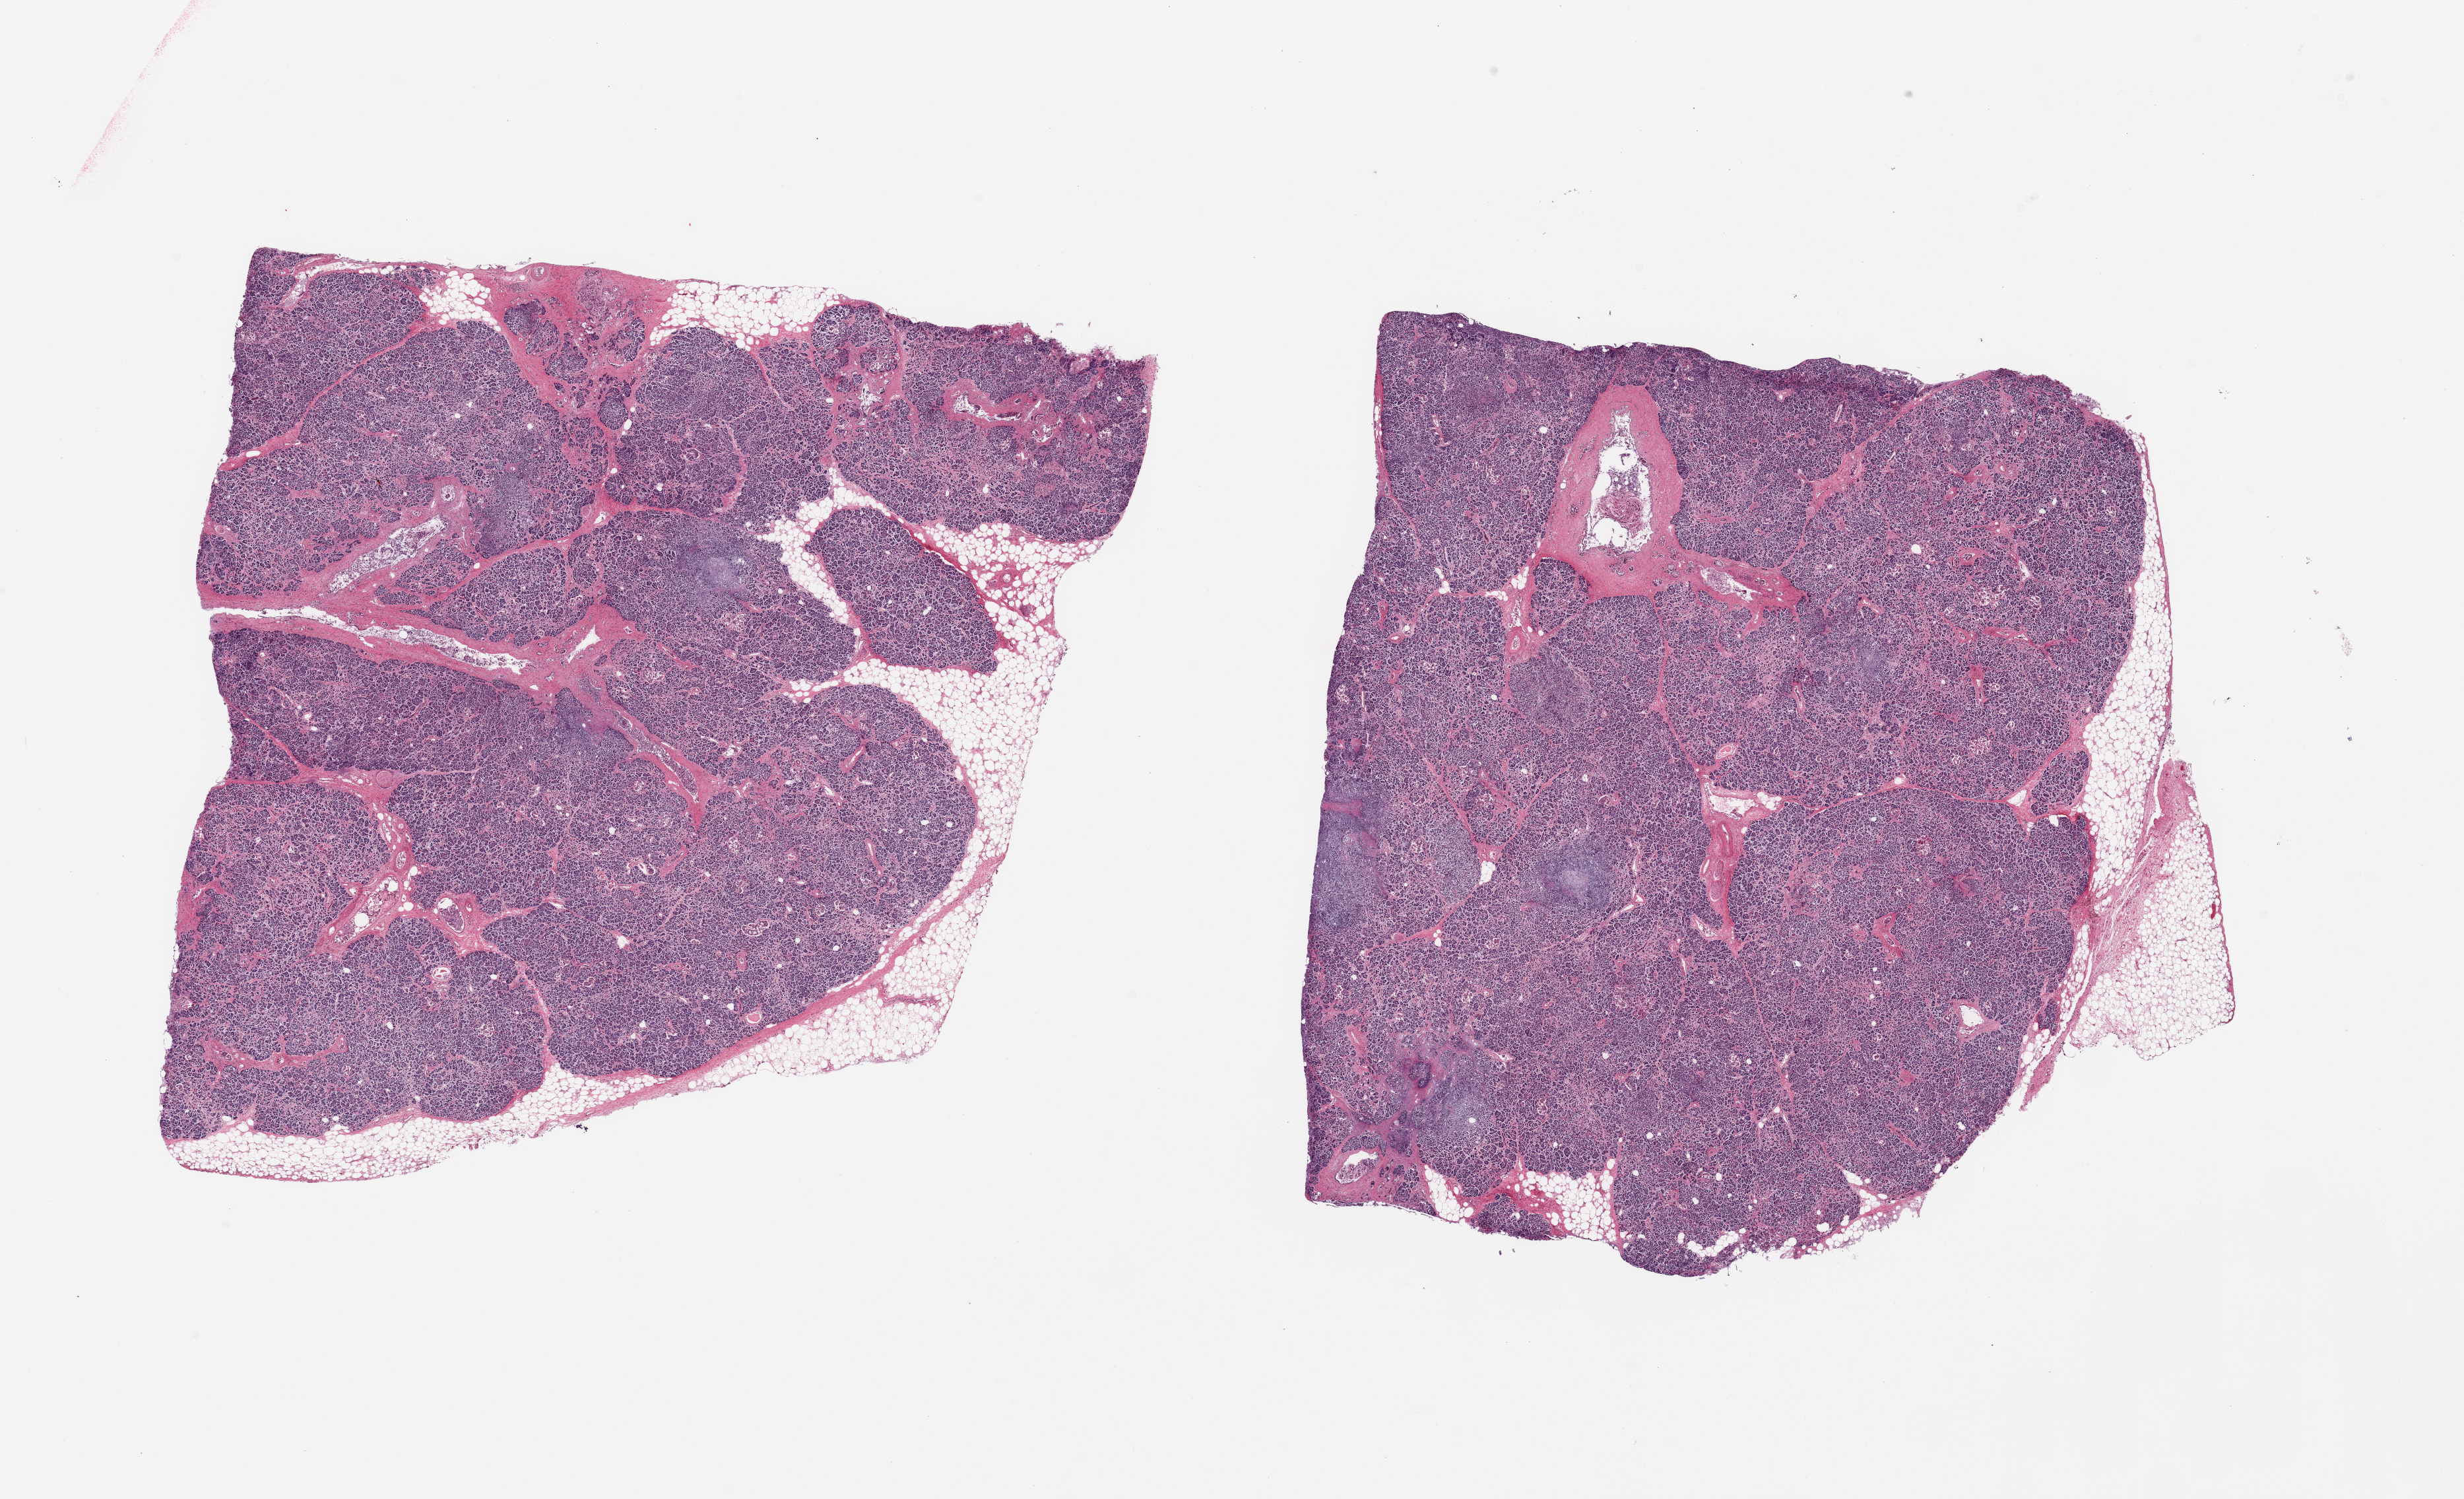
Hematoxylin and eosin (H&E) whole-slide image, low-resolution overview of the scanned area, about 29.5 x 18.0 mm. PAXgene-fixed paraffin-embedded (PFPE) section. Section of pancreas (target tissue). Tissue donor sample. Donor sex: male.
- review note (as recorded): 2 pieces; 15% and 10% external fat; interstitial fibrosis; moderately to severely autolyzed parenchyma; Langerhans islets present